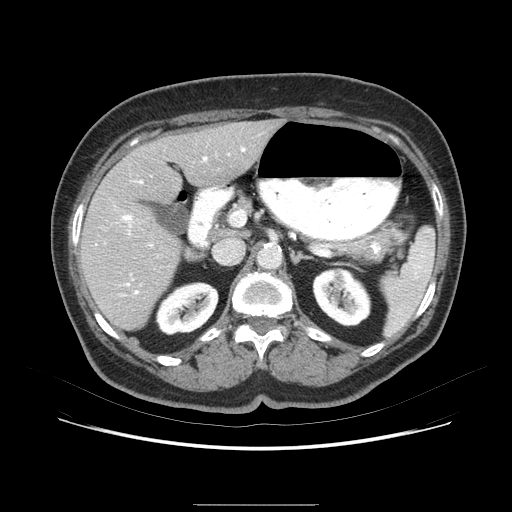
Contrast-enhanced abdominal CT (liver protocol), one axial slice. Position 40 of 79 along the scan axis. Soft-tissue window (W 400 / L 40 HU). 2.5 mm slice thickness. 512 × 512 image matrix, field of view 380 × 380 mm. Case-level facts recorded for this patient, not image findings: diagnosis: hepatocellular carcinoma (patient treated with transarterial chemoembolisation; whether this scan precedes or follows treatment is not stated here); TNM stage (as recorded): Stage-I; Child-Pugh class: A; tumour differentiation: poorly differentiated.
Structures marked on this image (semi-automatically segmented with operator editing):
- liver parenchyma outside the tumour (the mass and vessels are separate outlines, so this box may not span the whole liver): box from (x=78, y=120) to (x=286, y=338) px
- mass: (x=126, y=200)–(x=168, y=245)
- liver vessels: (x=118, y=144)–(x=259, y=288)